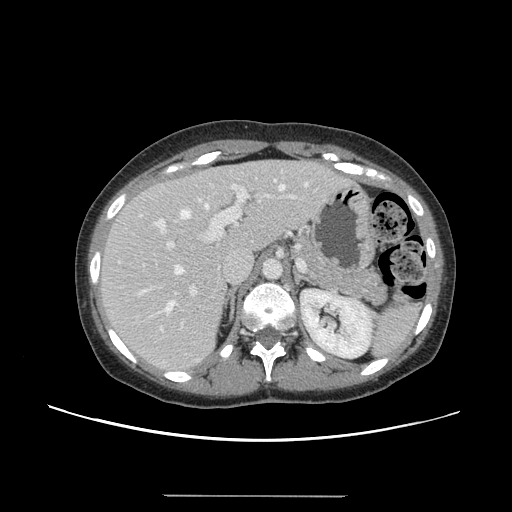
Contrast-enhanced abdominal CT, one axial slice; slice 93 of 144 in the series (ordered by position); 120 kVp; intravenous contrast given; soft-tissue window (W 400 / L 40 HU); 2.5 mm slice thickness; 512 × 512 image matrix, field of view 380 × 380 mm. Female patient, age 53 years. From the clinical record (not read from this slice): diagnosis: colorectal cancer liver metastases, imaged before liver resection; multiple liver metastases: yes; largest metastasis: 1.1 cm.
Structures marked on this image (expert manual segmentation):
- hepatic veins: bounding box [x1, y1, x2, y2] px = [140, 183, 308, 329]
- liver: [98, 161, 343, 372]
- planned liver remnant (the part of the liver to remain after resection): [98, 161, 311, 299]
- portal vein (with intrahepatic branches): [154, 179, 296, 296]